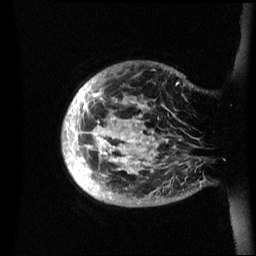
Breast MRI (dynamic contrast-enhanced), one sagittal slice. Slice 6 of 60 in the series (ordered by position). Dynamic contrast-enhanced series, image 2 of 3 at this slice position (ordered by acquisition). 1.5 T. TE 4.2 ms, TR 8.4 ms. 2.4 mm slice thickness. 256 × 256 image matrix, field of view 230 × 230 mm. Female patient, age 48 years.
Annotated regions visible in this slice (semi-automatically segmented with operator editing):
- analysis volume of interest (the breast-tissue region the enhancement analysis was run in; not a lesion): box from (x=62, y=61) to (x=202, y=207) px
- tumour enhancement mask (voxels above the 70 % enhancement threshold inside the analysis volume of interest): (x=63, y=82)–(x=179, y=189)